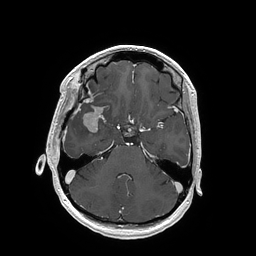
Brain MRI from a brain-tumour surgery series, one axial slice. Slice 115 of 202 in the series (ordered by position). T1-weighted post-contrast. 256 × 256 image matrix, field of view 250 × 250 mm. From the clinical record (not read from this slice): histopathology: Glioblastoma; WHO grade: 4; IDH mutation: no; tumour location: Right Insular.
Annotated regions visible in this slice (outlined manually by an expert reader):
- tumour: bounding box (x1, y1, x2, y2) in pixels: (83, 106, 102, 132)